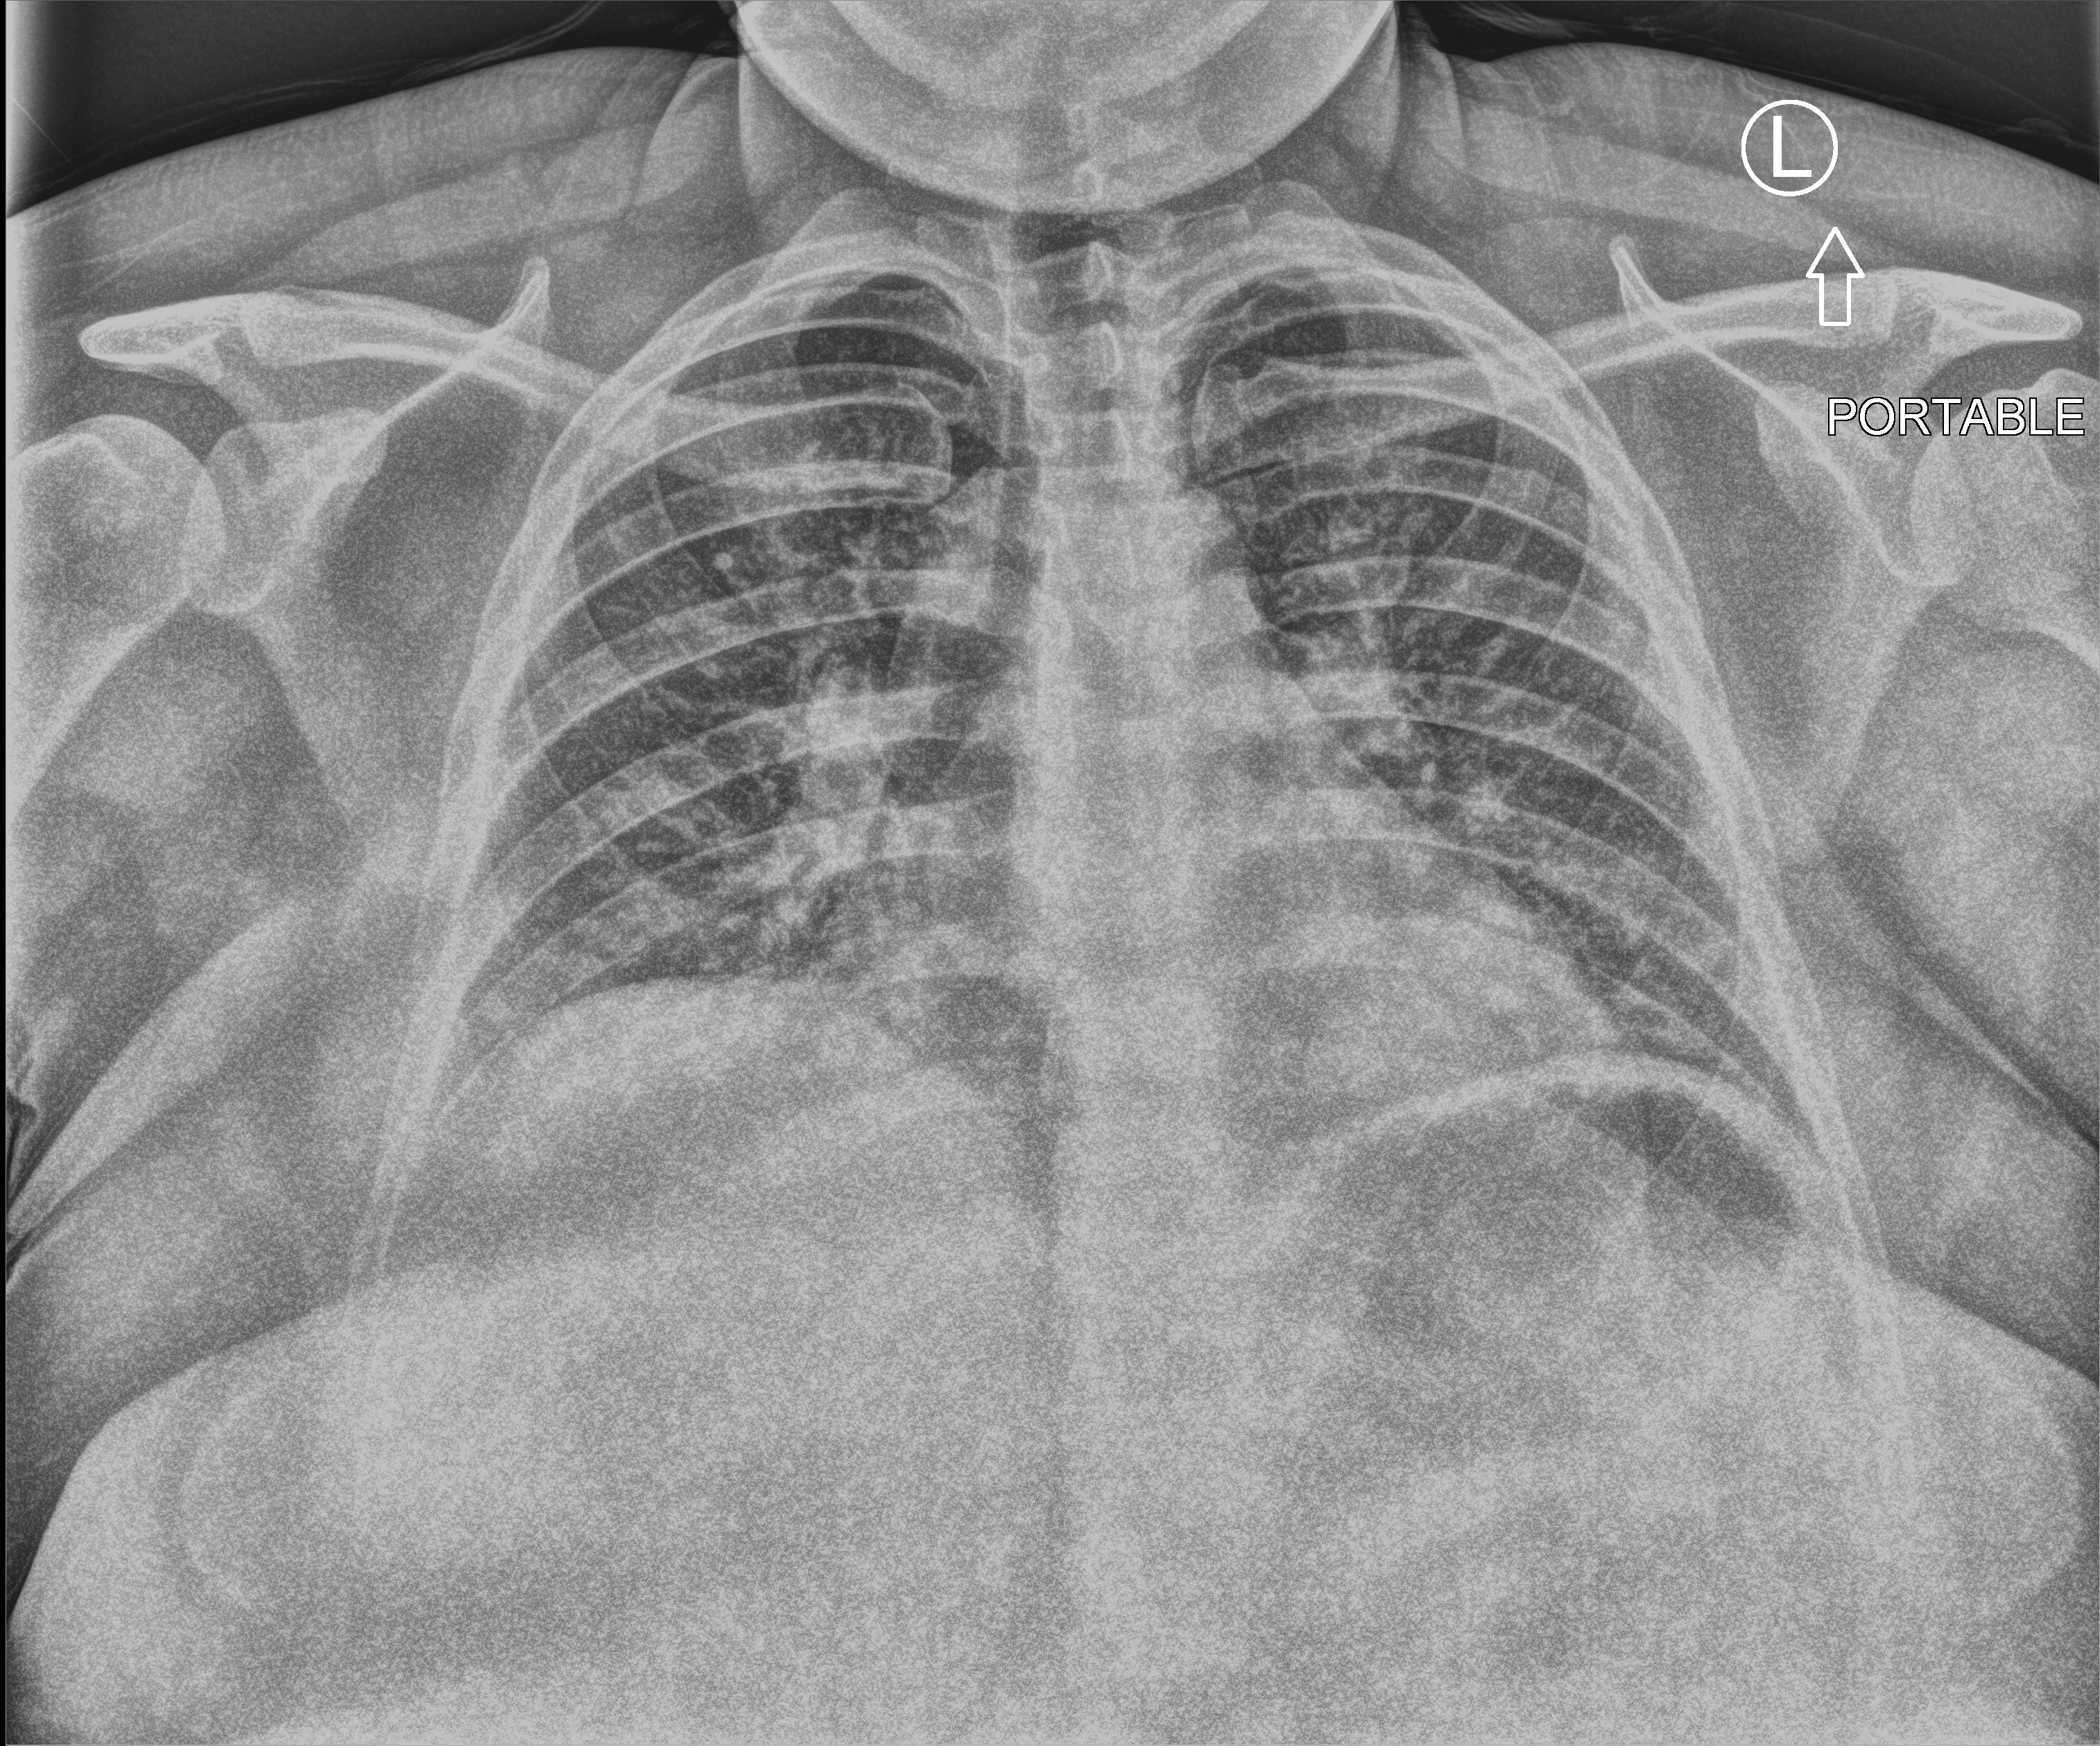
Chest X-ray (portable), anteroposterior (AP) projection. Female patient hospitalised with COVID-19, age 18–59 years.
From the hospital-stay record, not from the radiograph (when in the stay this image was taken is not recorded): other chronic lung disease (admission record): no; admitted to intensive care during this hospital stay: no; mechanically ventilated during this hospital stay: no.